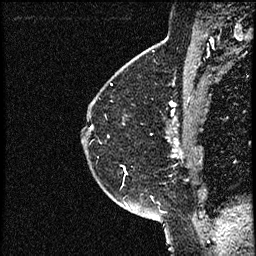
Breast MRI (dynamic contrast-enhanced), one sagittal slice. Position 41 of 52 along the scan axis. Dynamic contrast-enhanced study with each time point stored as its own series, time point 2 of 3 at this slice position (early post-contrast, ordered by acquisition time). 1.5 T. TE 4.2 ms, TR 17.6 ms. 256 × 256 image matrix, field of view 200 × 200 mm. Female patient, age 49 years. Case-level facts recorded for this patient, not image findings: setting: breast cancer imaged before/during neoadjuvant chemotherapy; receptor status: HER2-positive.
Outlined on this slice (semi-automatic segmentation, software-assisted and operator-edited):
- analysis volume of interest (the breast-tissue region the enhancement analysis was run in; not a lesion): bounding box [x1, y1, x2, y2] px = [85, 65, 182, 175]
- tumour enhancement mask (voxels above the 100 % enhancement threshold inside the analysis volume of interest): [172, 103, 181, 156]